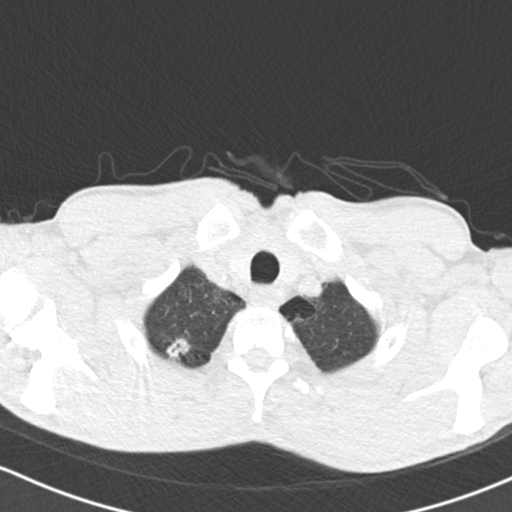
Low-dose screening chest CT, one axial slice. Position 128 of 150 along the scan axis. 120 kVp. Lung window (W 1500 / L -600 HU). 2 mm slice thickness. 512 × 512 image matrix, field of view 312 × 312 mm.
Structures marked on this image (expert manual segmentation):
- lesion 1 (tumor, upper lobe of right lung): bounding box [x1, y1, x2, y2] px = [166, 338, 190, 358]